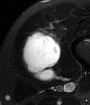
MRI of an extremity soft-tissue mass, one axial slice; position 19 of 65 along the scan axis; T2-weighted fat-saturated; MR volume resampled by the dataset authors to the PET/CT grid (not the native acquisition matrix); 3.27 mm slice thickness; 90 × 105 image matrix, field of view 88 × 103 mm. Male patient. Case-level facts recorded for this patient, not image findings: histological type: mixoid liposarcoma; grade: low; site of the primary tumour: left thigh.
Structures marked on this image (expert contour drawn on MRI and transferred to this co-registered scan by the dataset authors):
- gross tumour volume (mass): bounding box (x1, y1, x2, y2) in pixels: (20, 32, 62, 81)